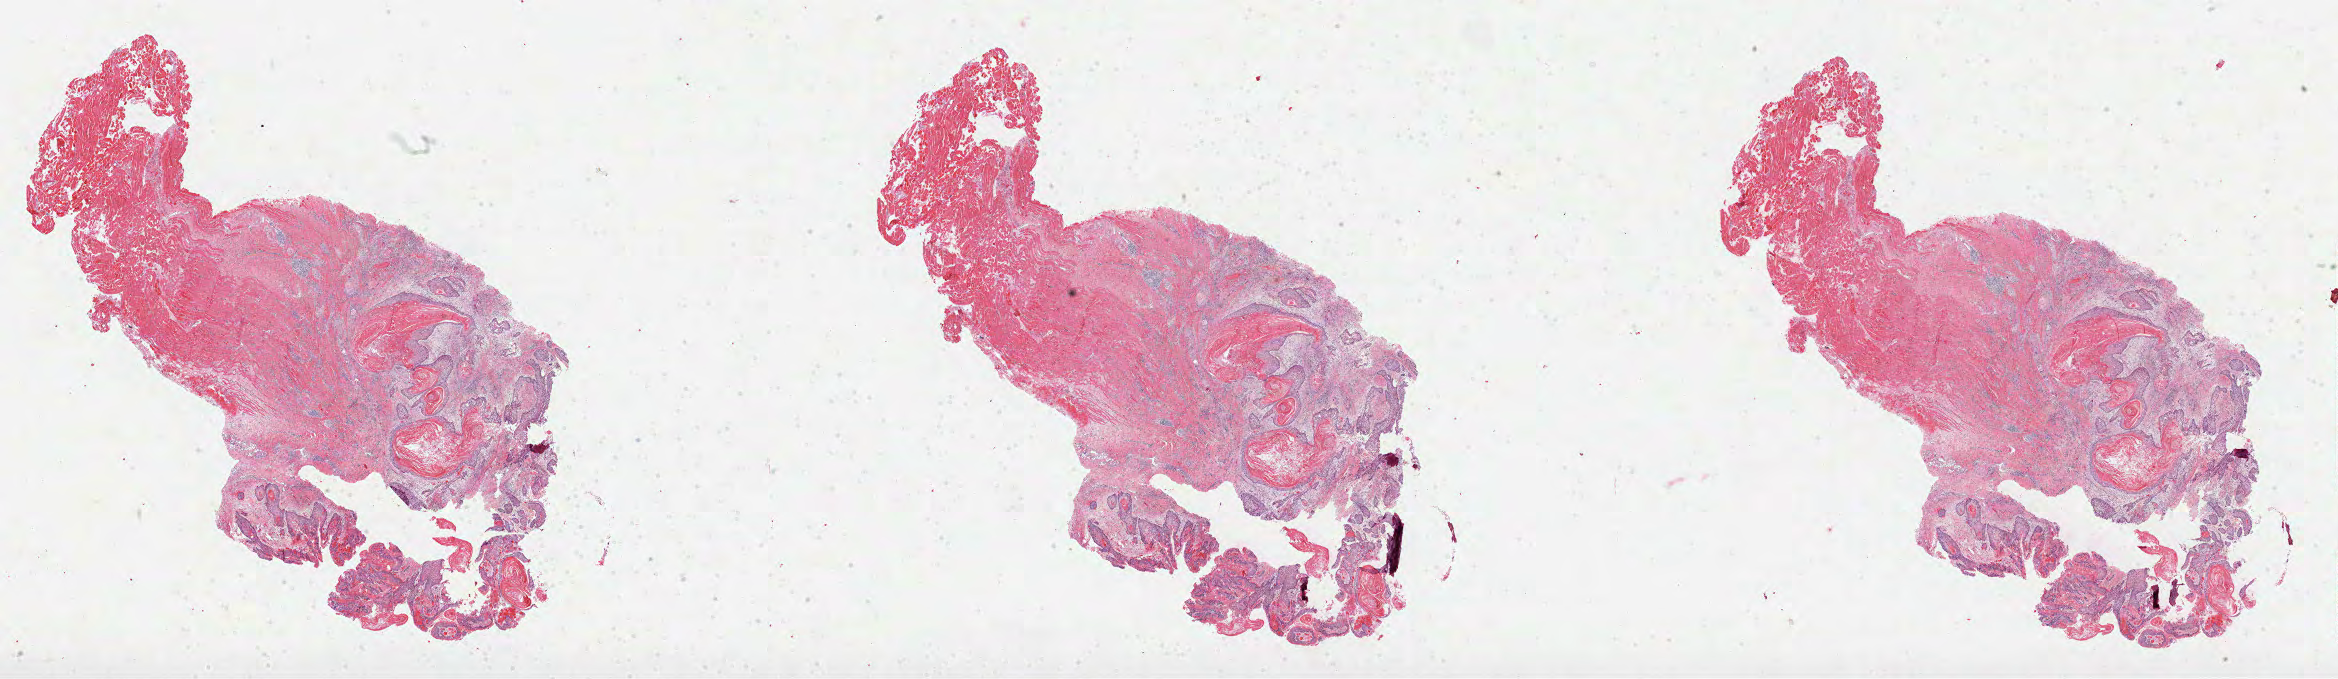
Whole-slide histology image, H&E-stained, whole scanned area (about 37.7 x 11.0 mm, from a 40x scan) shown as a low-resolution overview, formalin-fixed paraffin-embedded (FFPE) diagnostic section, primary tumour sample from the head and neck. Female, age 79 years at initial diagnosis. Histologic grade: G2 (moderately differentiated).
Histologic diagnosis: Squamous cell carcinoma, NOS (mouth, NOS). AJCC pathologic stage: IVA (6th edition).